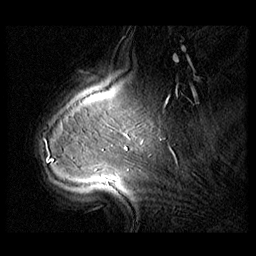
Breast MRI (dynamic contrast-enhanced), one sagittal slice; slice 21 of 104 in the series (ordered by position); 3 images stored at this slice position (order not interpretable as contrast timing); 1.5 T; TE 1.3 ms, TR 5.5 ms; 3 mm slice thickness; 256 × 256 image matrix, field of view 220 × 220 mm. Patient: female, 54 years. Case-level facts recorded for this patient, not image findings: setting: breast cancer imaged before/during neoadjuvant chemotherapy; receptor status: HR-positive, HER2-negative.
Outlined on this slice (semi-automatic segmentation, software-assisted and operator-edited):
- analysis volume of interest (the breast-tissue region the enhancement analysis was run in; not a lesion): box from (x=36, y=127) to (x=104, y=182) px
- tumour enhancement mask (voxels above the 140 % enhancement threshold inside the analysis volume of interest): (x=51, y=159)–(x=53, y=161)